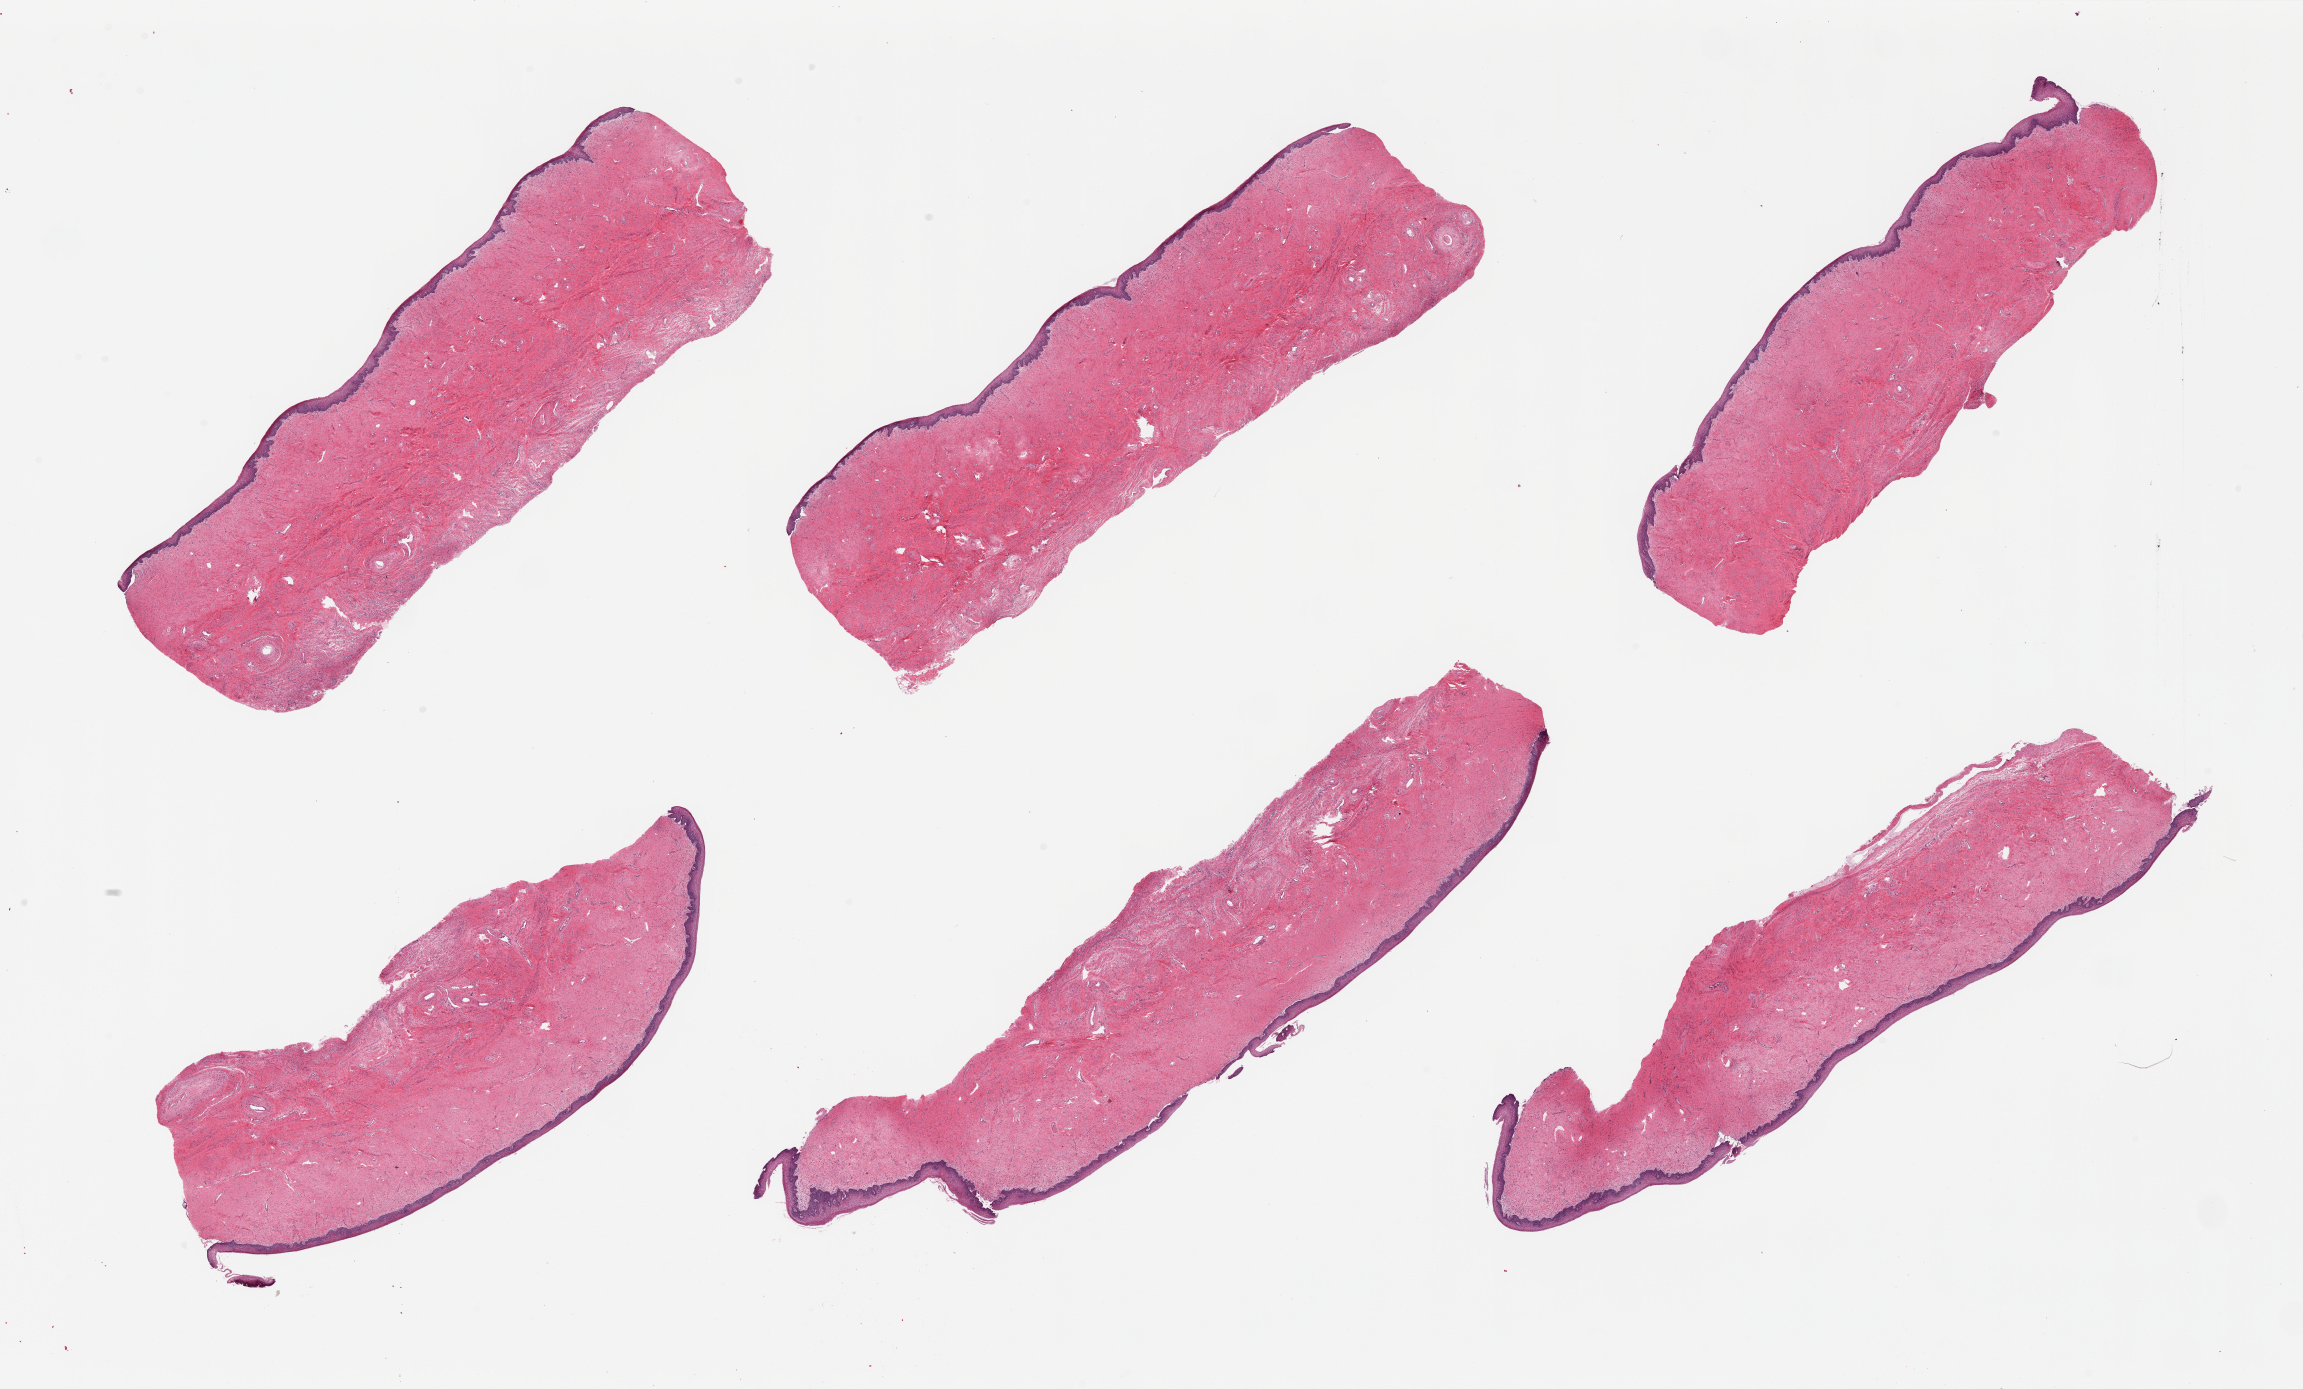
Whole-slide image, haematoxylin and eosin stain, shown as a low-resolution overview of the whole scanned area (about 36.4 x 22.0 mm, acquisition: 20x scan), PAXgene-fixed paraffin-embedded (PFPE) section, sampled site (target tissue): vagina, donor tissue sample. Female donor.
Review note (as recorded): 6 pieces, squamous mucosa is ~150-200 microns.